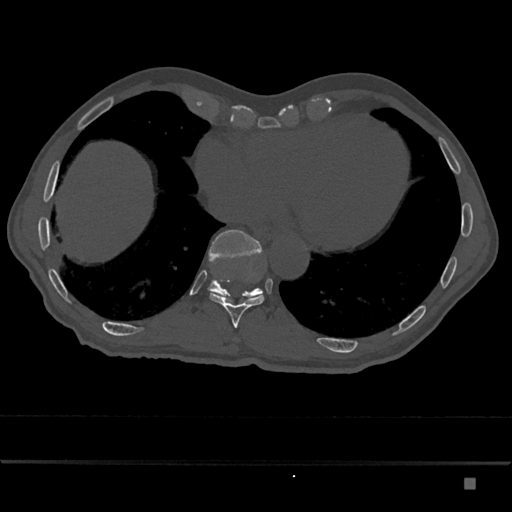
CT including the spine, one axial slice. Bone window (W 1800 / L 400 HU). 0.5 mm slice thickness. 512 × 512 image matrix, field of view 390 × 390 mm. Male patient, age 72 years. From the clinical record (not read from this slice): primary cancer: prostate.
Annotated regions visible in this slice (semi-automatic segmentation, software-assisted and operator-edited):
- T10 vertebra: bounding box <210,293,265,328> (left, top, right, bottom; pixels)
- T11 vertebra: <208,230,263,301>